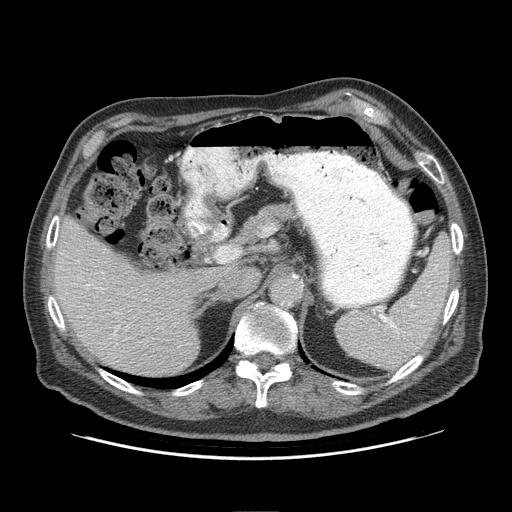
Contrast-enhanced abdominal CT (liver protocol), one axial slice; position 58 of 95 along the scan axis; reconstruction kernel STANDARD; soft-tissue window (W 400 / L 40 HU); 512 × 512 image matrix. Case-level facts recorded for this patient, not image findings: diagnosis: hepatocellular carcinoma (patient treated with transarterial chemoembolisation; whether this scan precedes or follows treatment is not stated here); TNM stage (as recorded): Stage-IVB; Child-Pugh class: A; tumour differentiation: well differentiated.
Annotated regions visible in this slice (semi-automatic segmentation, software-assisted and operator-edited):
- liver parenchyma outside the tumour (the mass and vessels are separate outlines, so this box may not span the whole liver): bounding box <54,218,217,374> (left, top, right, bottom; pixels)
- liver vessels: <88,284,117,314>